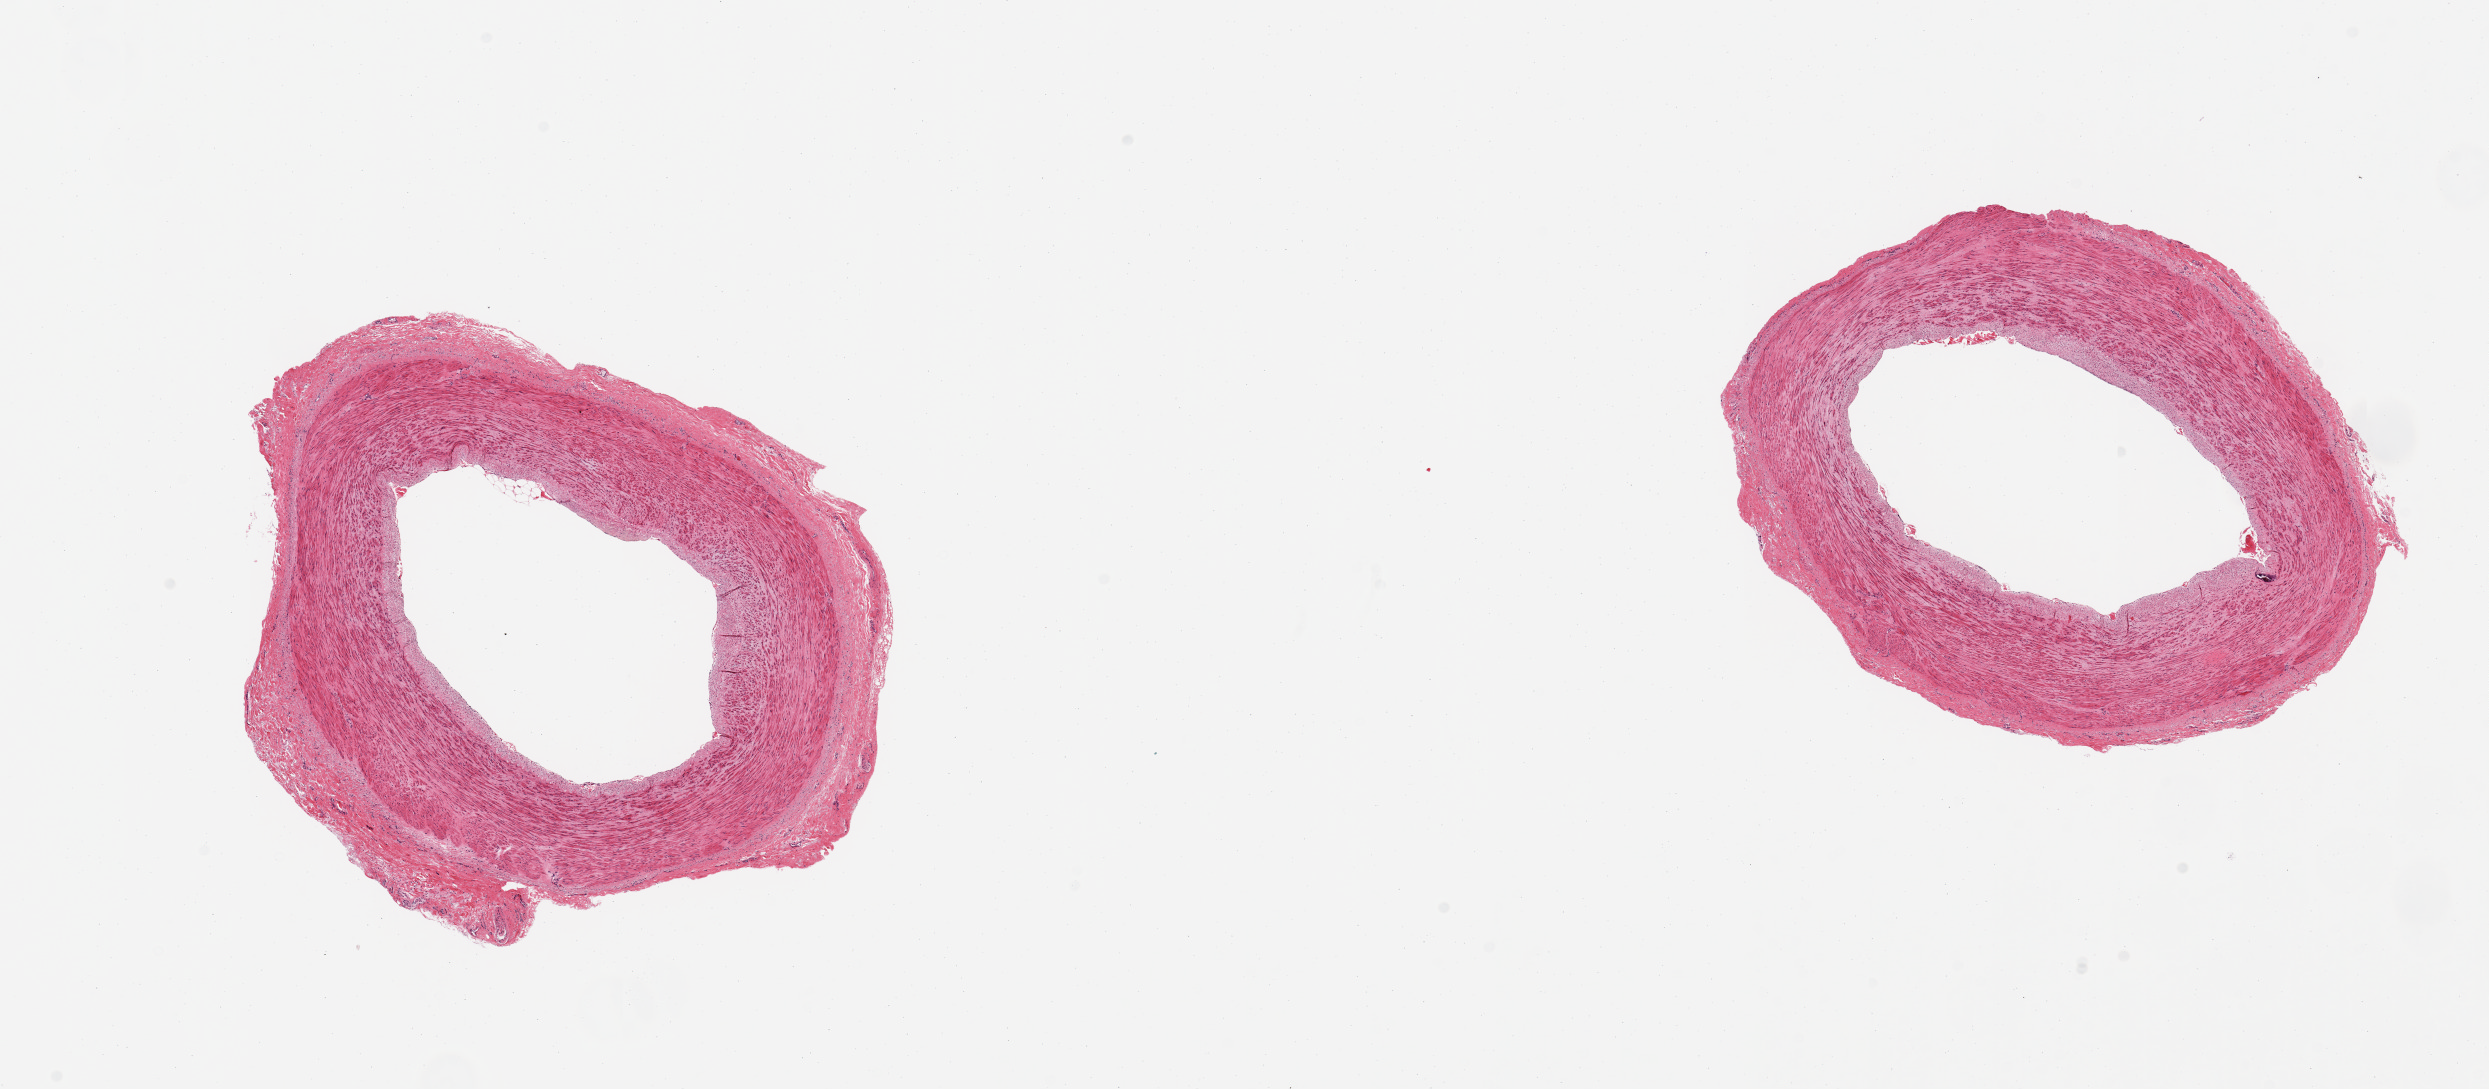
H&E whole-slide image, low-resolution overview of the scanned area, about 19.7 x 8.6 mm; PAXgene-fixed, paraffin-embedded tissue; sampled site (target tissue): tibial artery; tissue donor sample. Donor: male.
Reviewer comment on this tissue sample: 2 pieces; well trimmed; no plaques; minute calcium deposit.